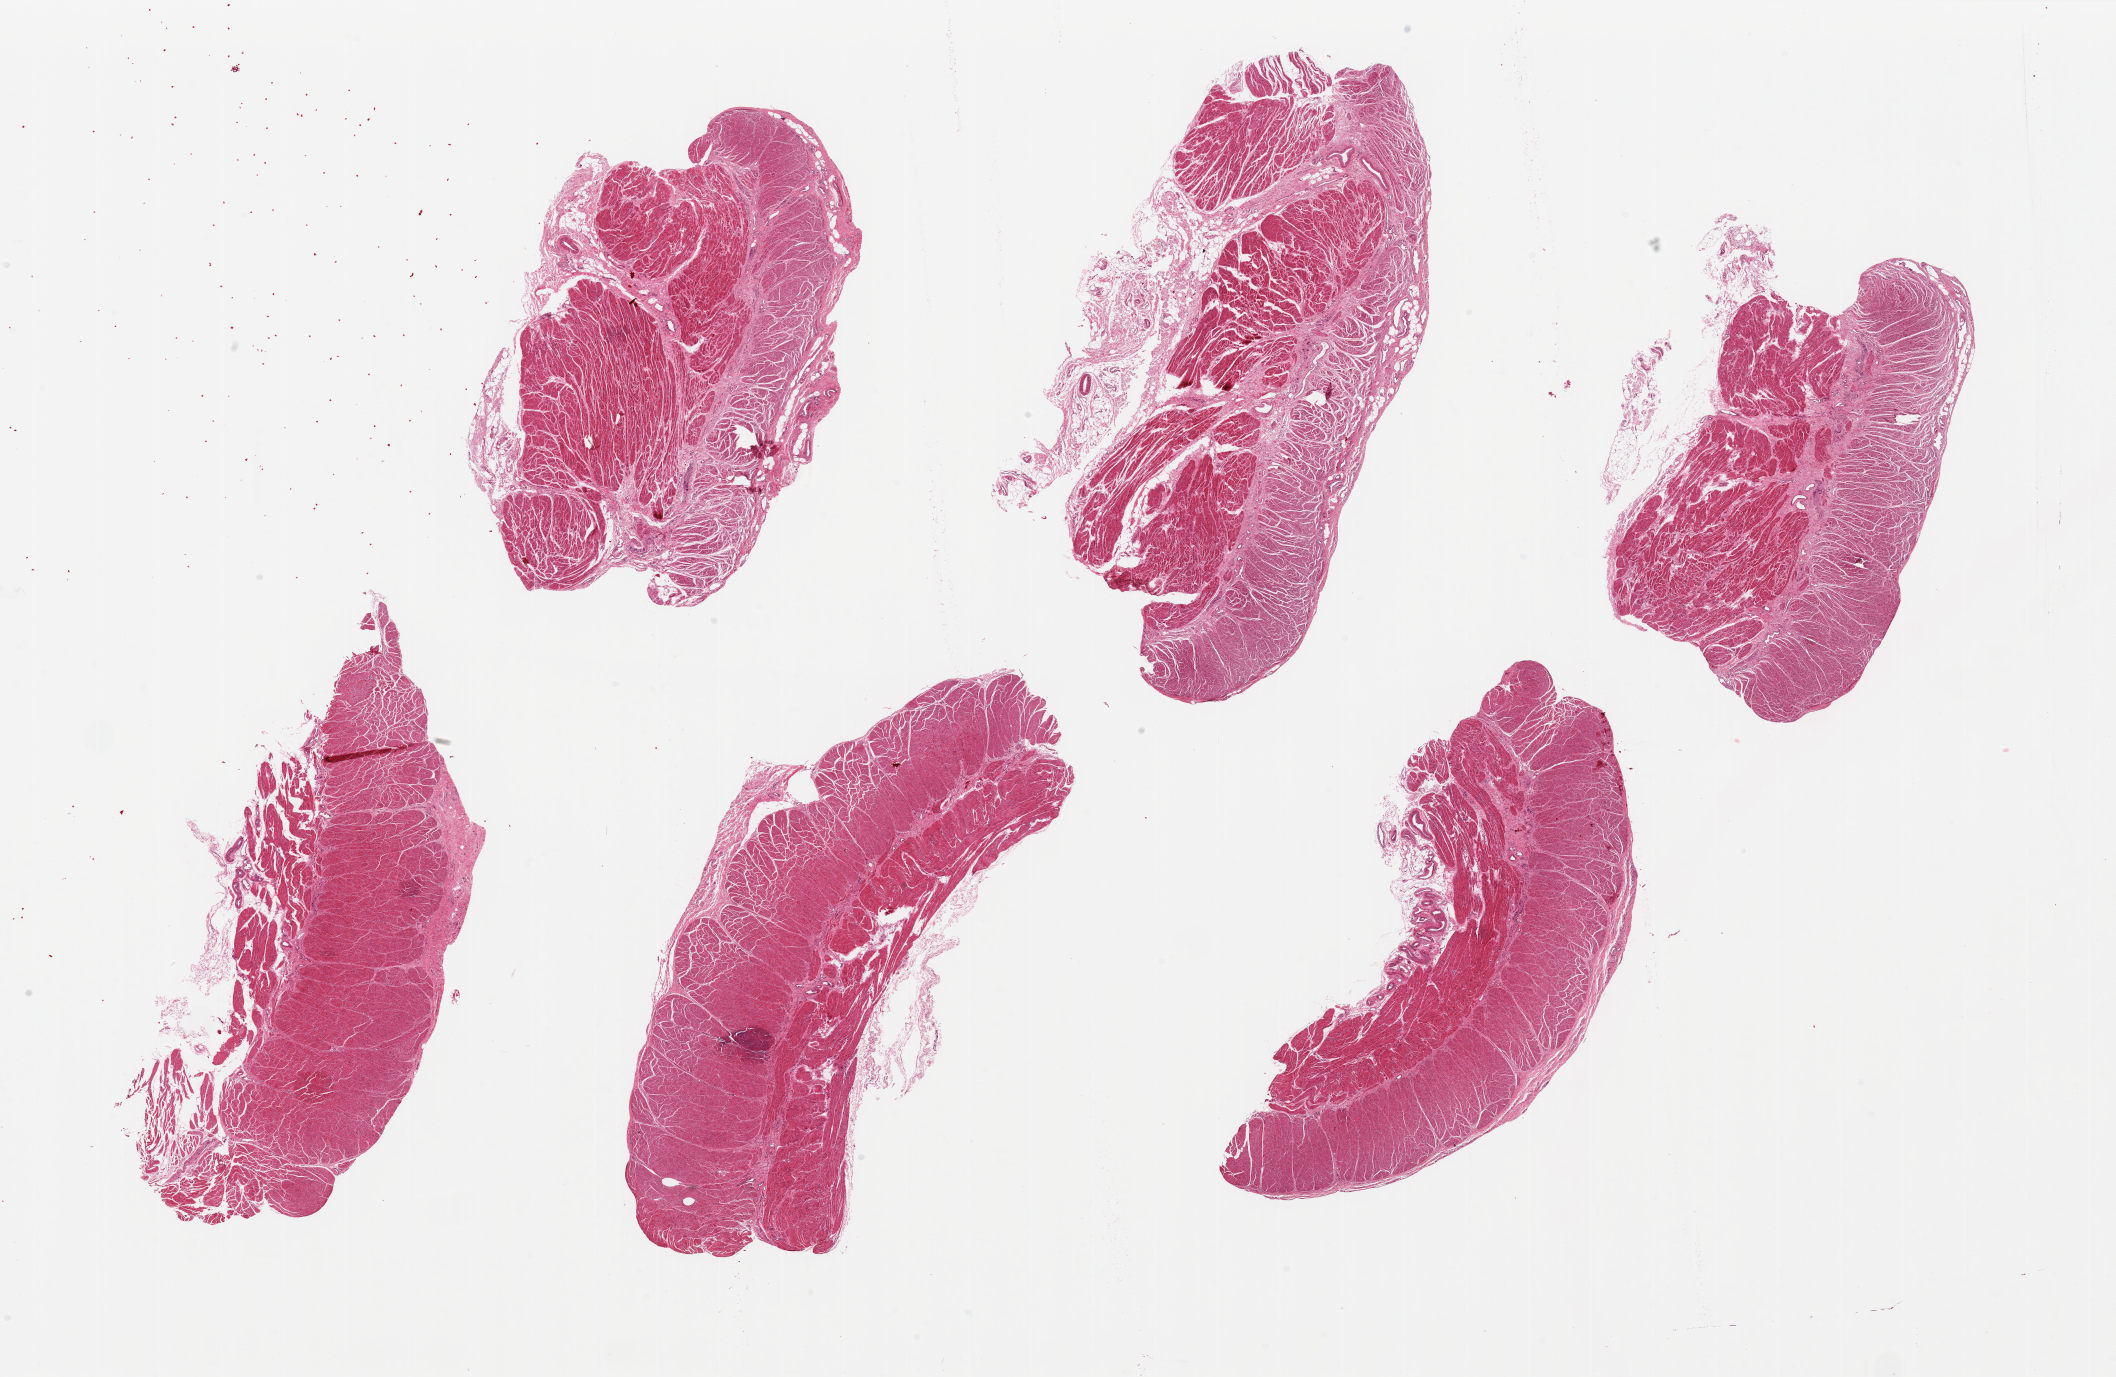
Whole-slide image, H&E stain, a low-resolution overview of the entire scanned area, about 33.5 x 21.8 mm. PAXgene-fixed paraffin-embedded (PFPE) section. Section of gastroesophageal junction (target tissue). Tissue donor sample.
Reviewer comment on this tissue sample: 6 pieces ~10x4mm. All muscle, good specimens.